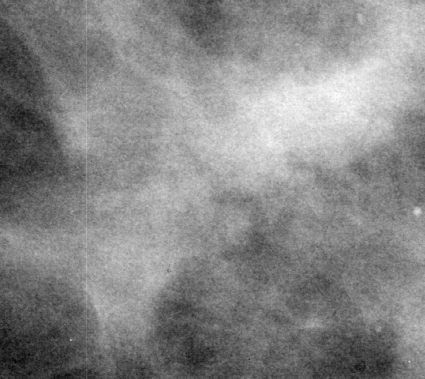
Region of interest cut from a scanned film mammogram (one marked finding), right breast, CC view, BI-RADS breast density category 1 (scale 1–4).
Mass, shape irregular / architectural distortion, margins ill defined / spiculated; BI-RADS assessment category 4; pathology (as recorded): malignant.